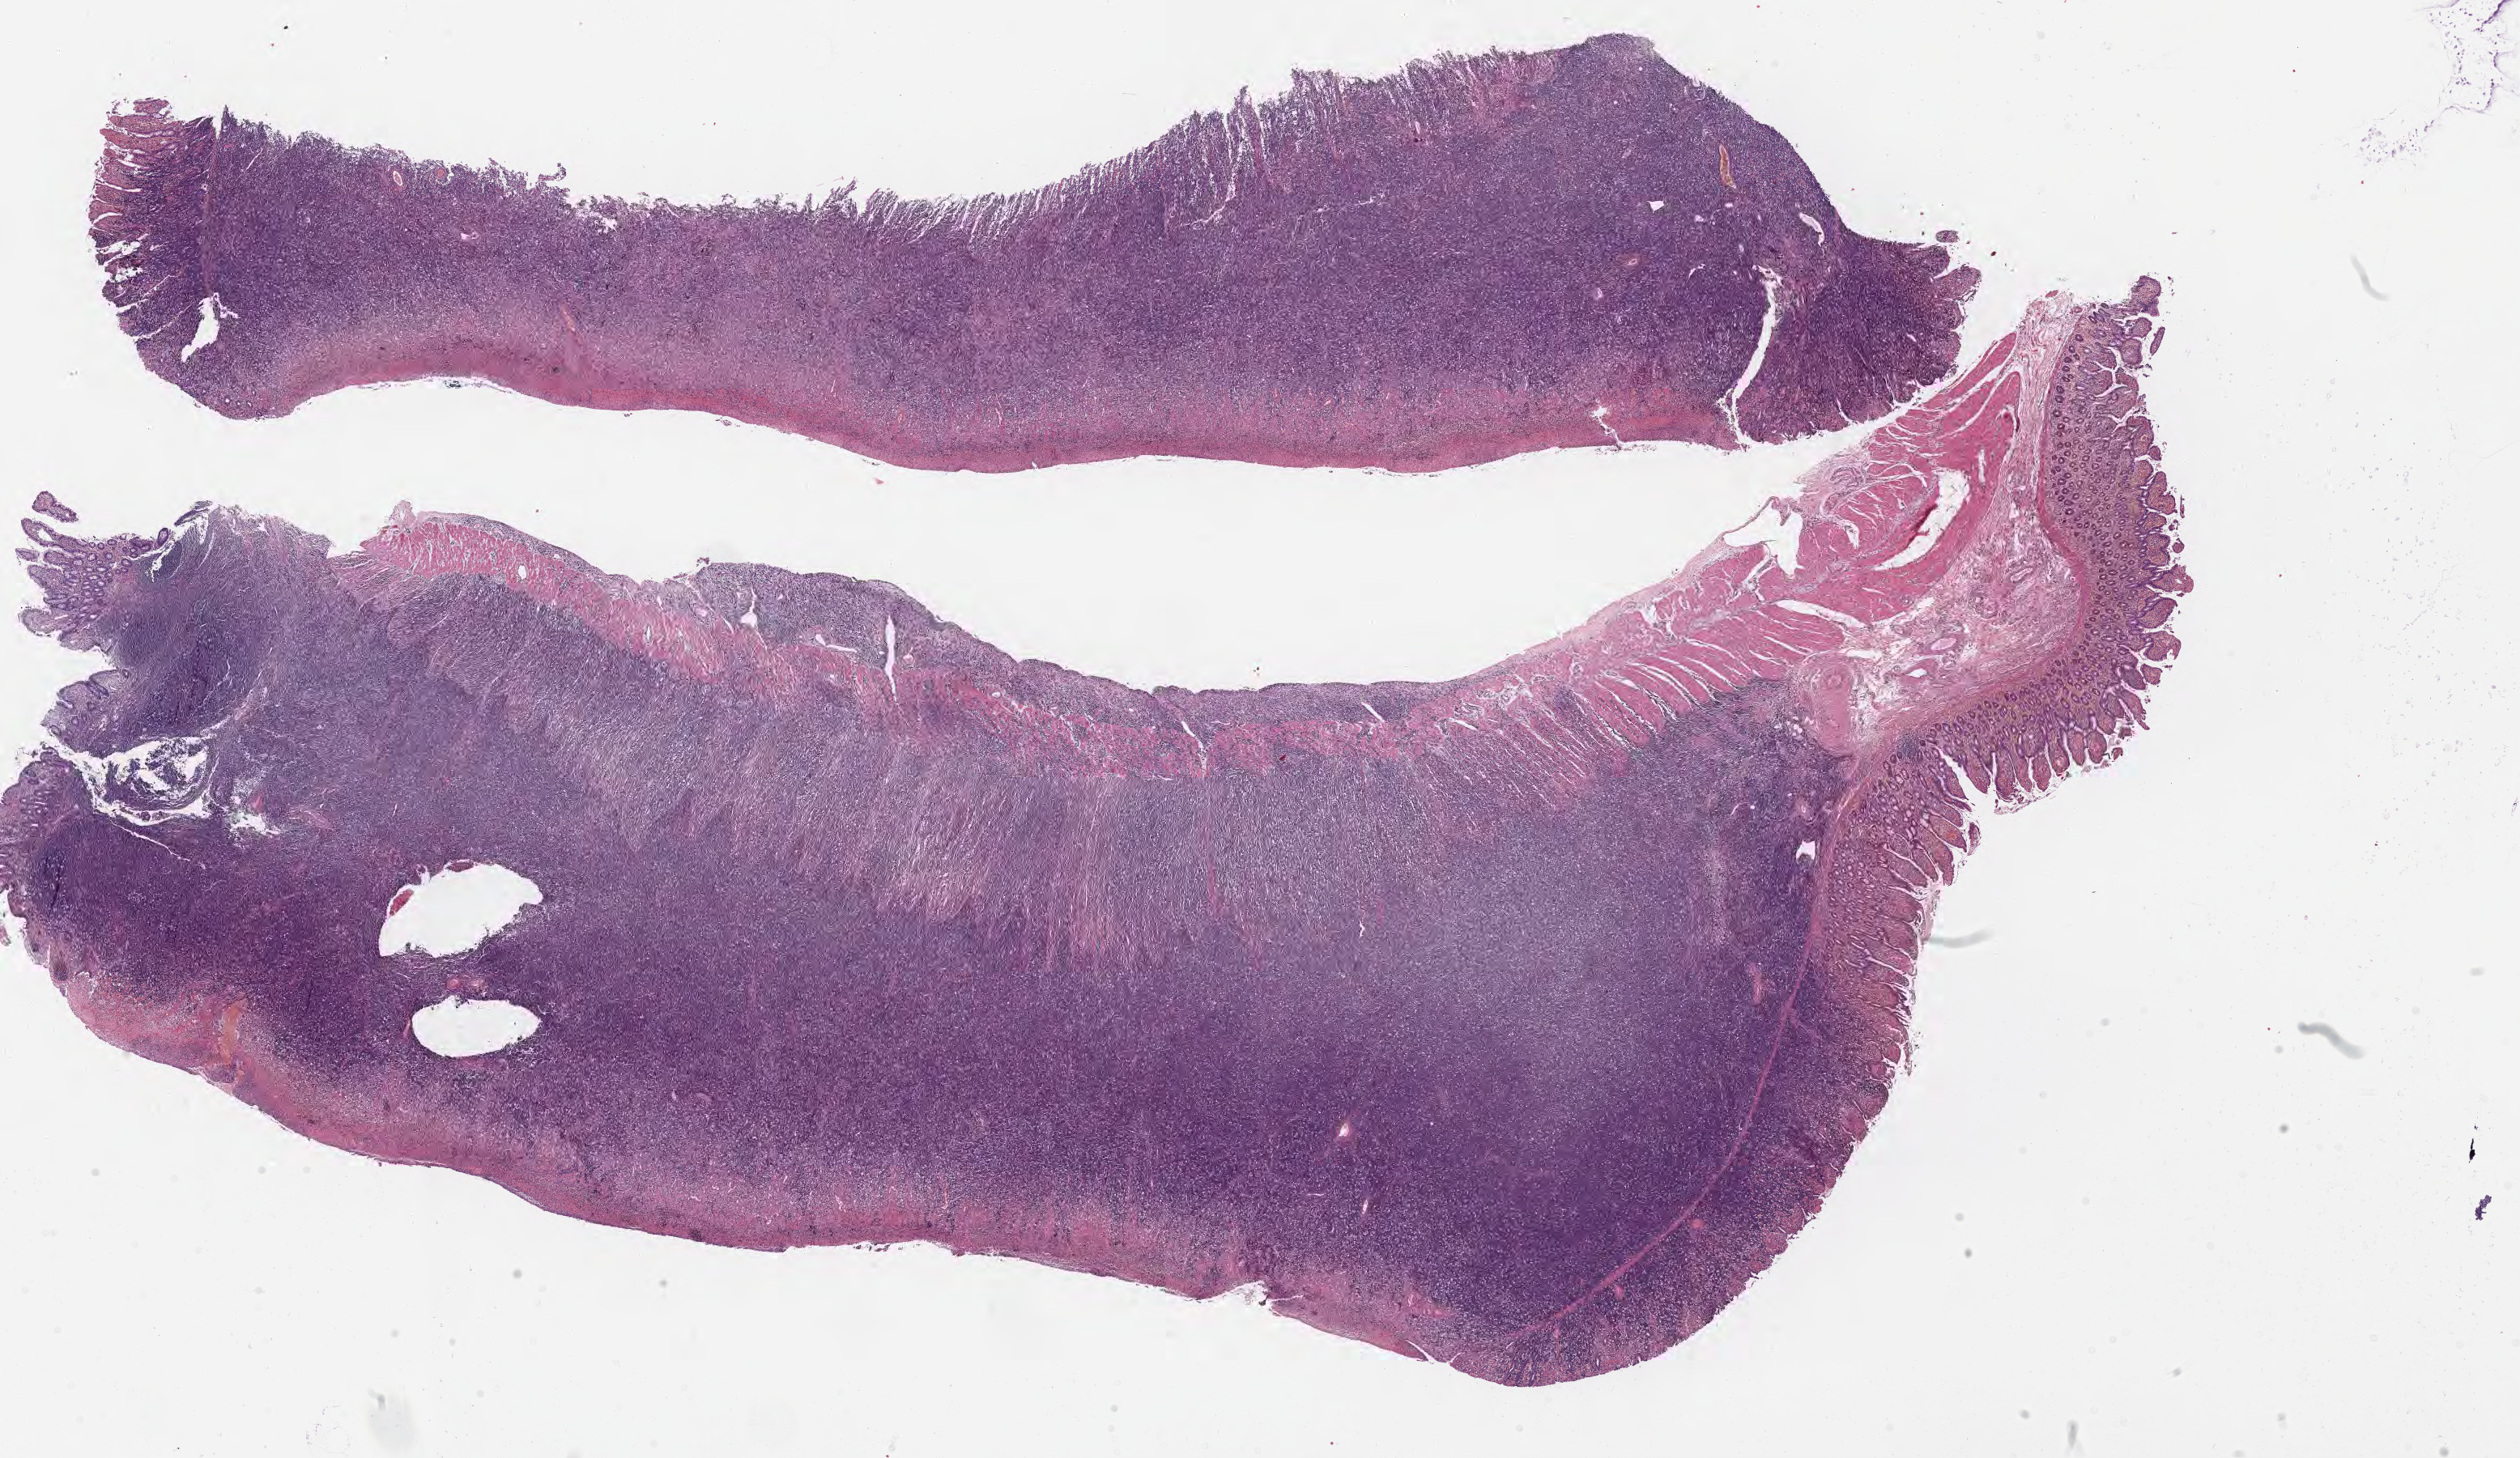
Digitized H&E-stained section, low-resolution overview of the scanned area, about 25.2 x 14.6 mm; tumor tissue. Female patient, aged 27.
* diagnosis: Burkitt lymphoma, NOS